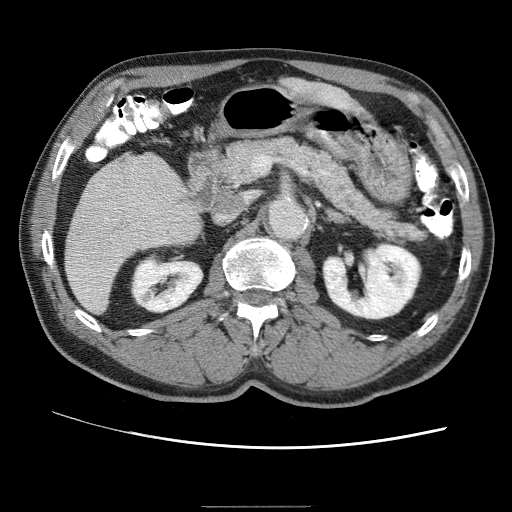
Contrast-enhanced abdominal CT (liver protocol), one axial slice; slice 17 of 75 in the series (ordered by position); reconstruction kernel STANDARD; 120 kVp; one of 2 acquisitions stored at this slice position; soft-tissue window (W 400 / L 40 HU); 2.5 mm slice thickness; 512 × 512 image matrix, field of view 360 × 360 mm. From the clinical record (not read from this slice): diagnosis: hepatocellular carcinoma (patient treated with transarterial chemoembolisation; whether this scan precedes or follows treatment is not stated here); TNM stage (as recorded): Stage-II; Child-Pugh class: A; tumour differentiation: well differentiated; tumour size: 2 cm.
Outlined on this slice (semi-automatic segmentation, software-assisted and operator-edited):
- liver parenchyma outside the tumour (the mass and vessels are separate outlines, so this box may not span the whole liver): box from (x=66, y=158) to (x=189, y=310) px
- liver vessels: (x=86, y=168)–(x=133, y=275)